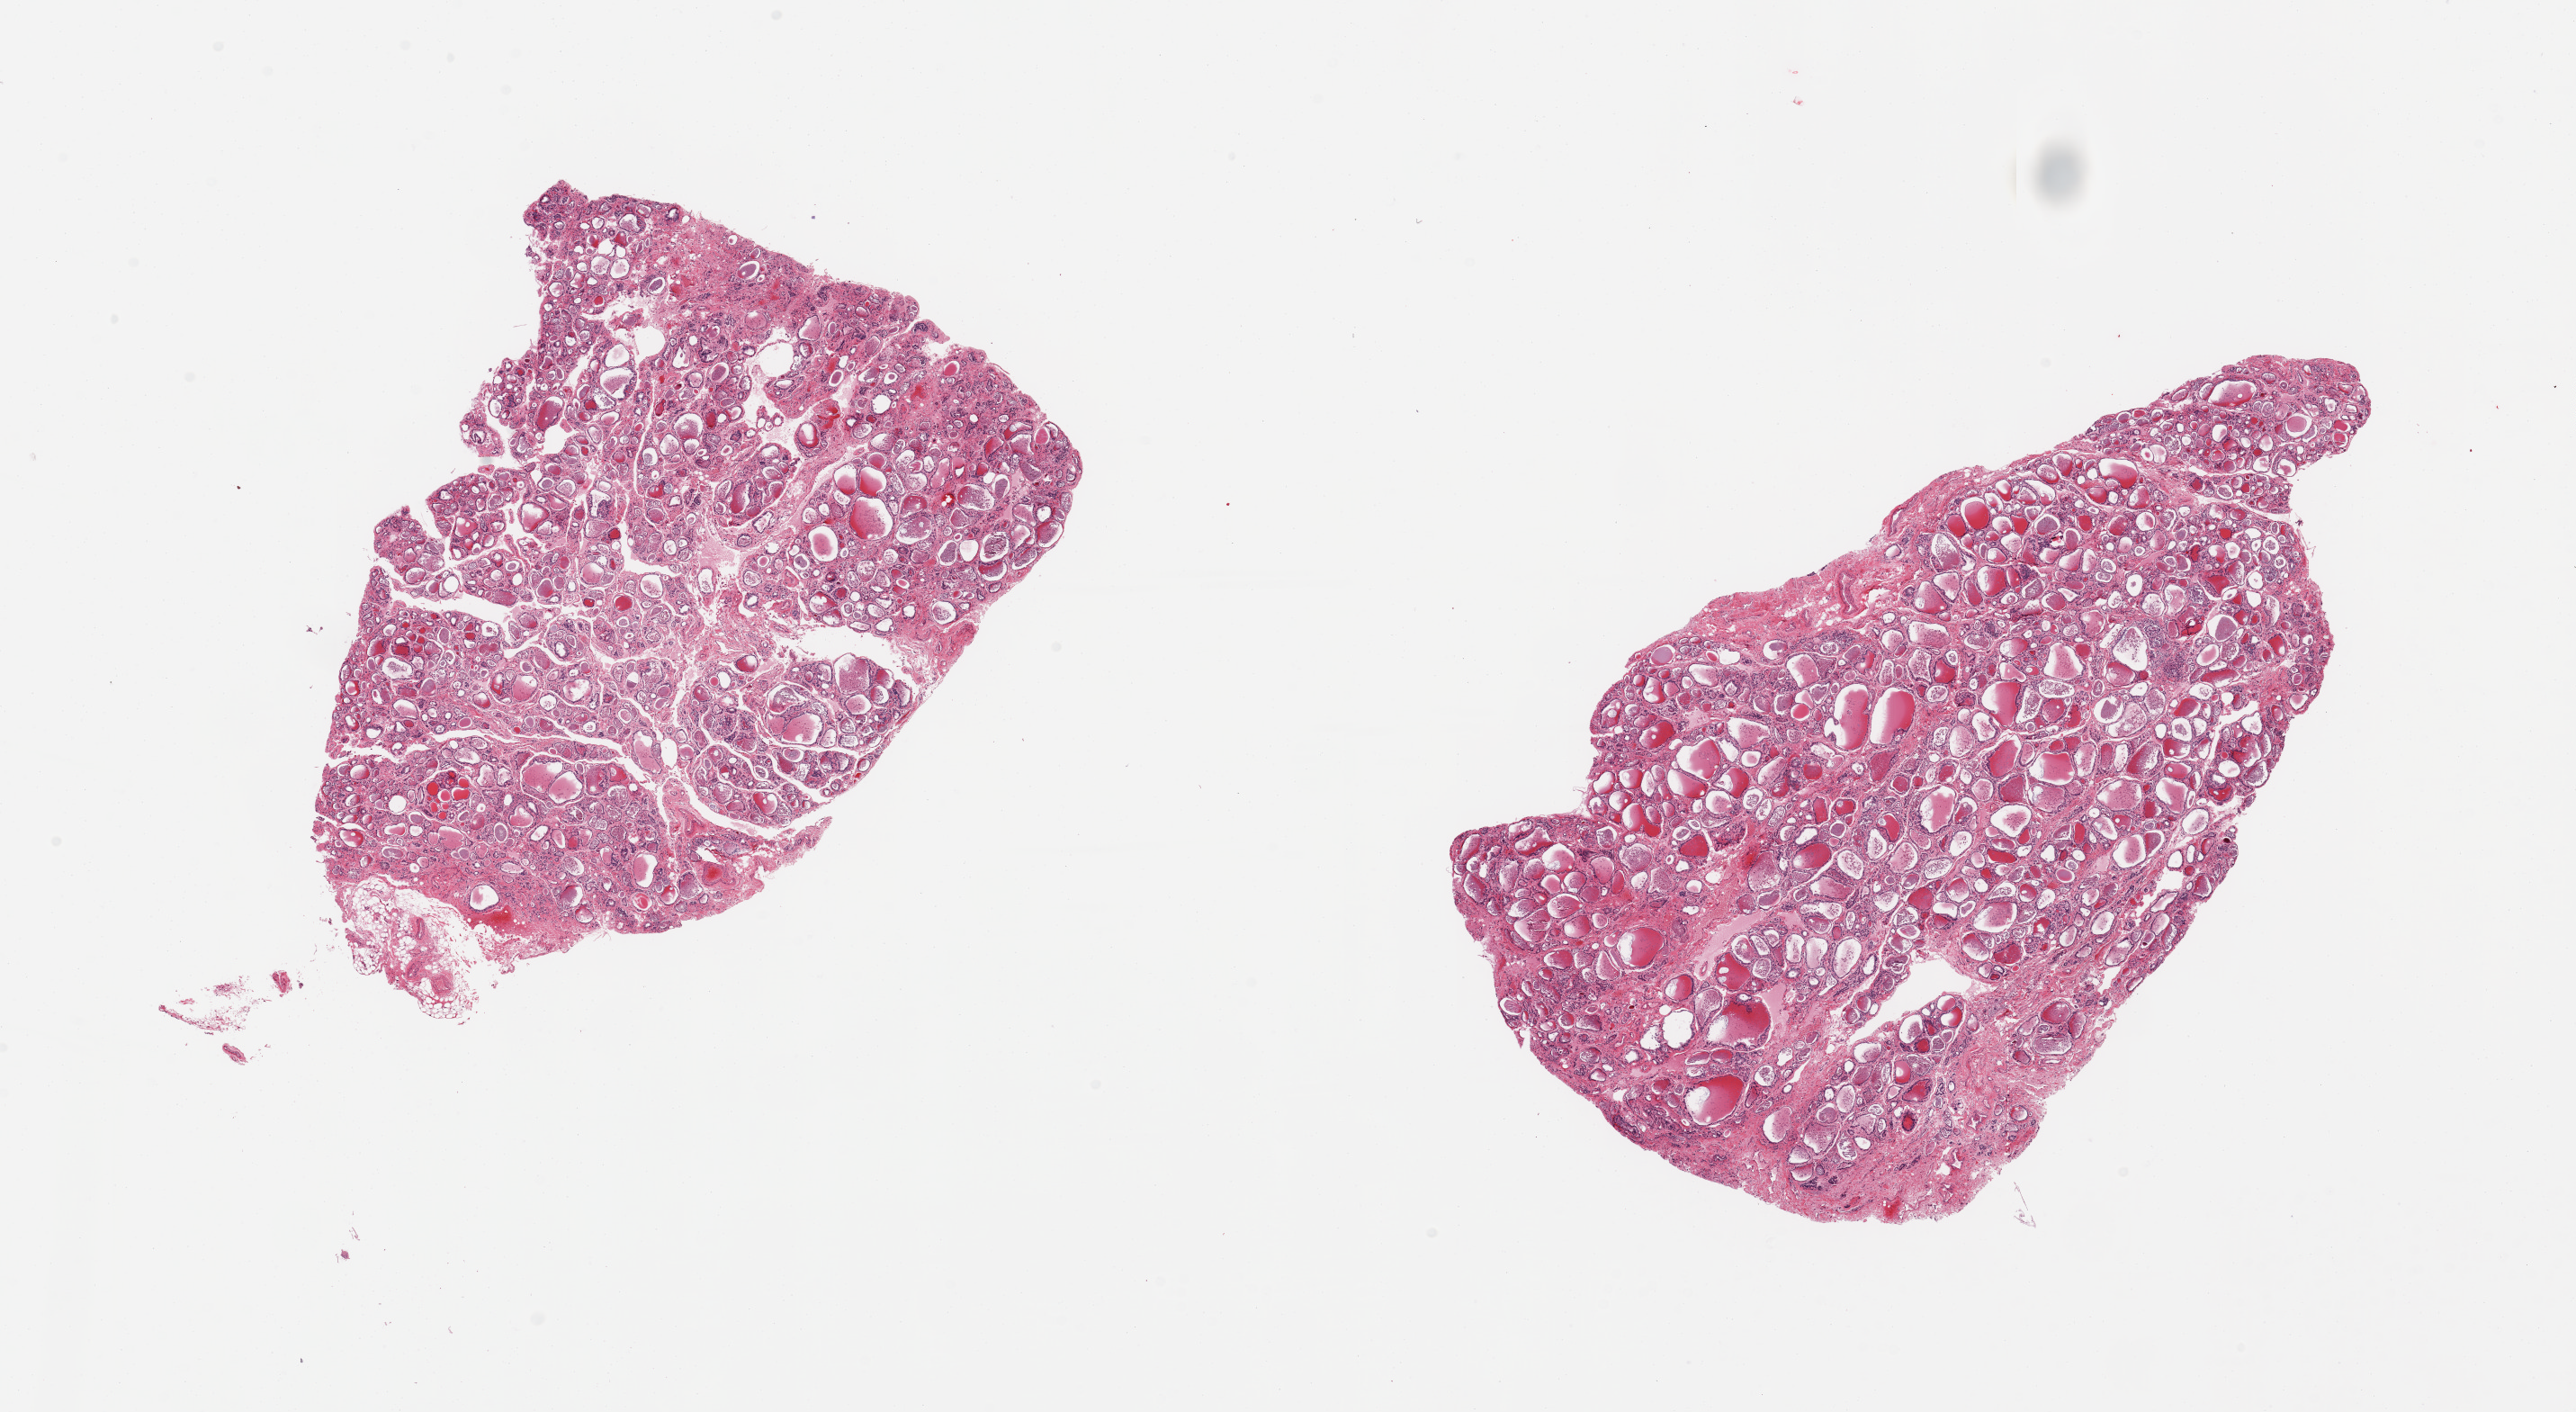
Digitized hematoxylin and eosin (H&E)-stained section, shown as a low-resolution overview of the whole scanned area (about 22.6 x 12.4 mm, from a 20x scan), PAXgene-fixed paraffin-embedded (PFPE) section, target tissue: thyroid, donor tissue sample. Donor: male.
Pathologist's review note for this sample: 2 pieces; some interstitial fibrosis.